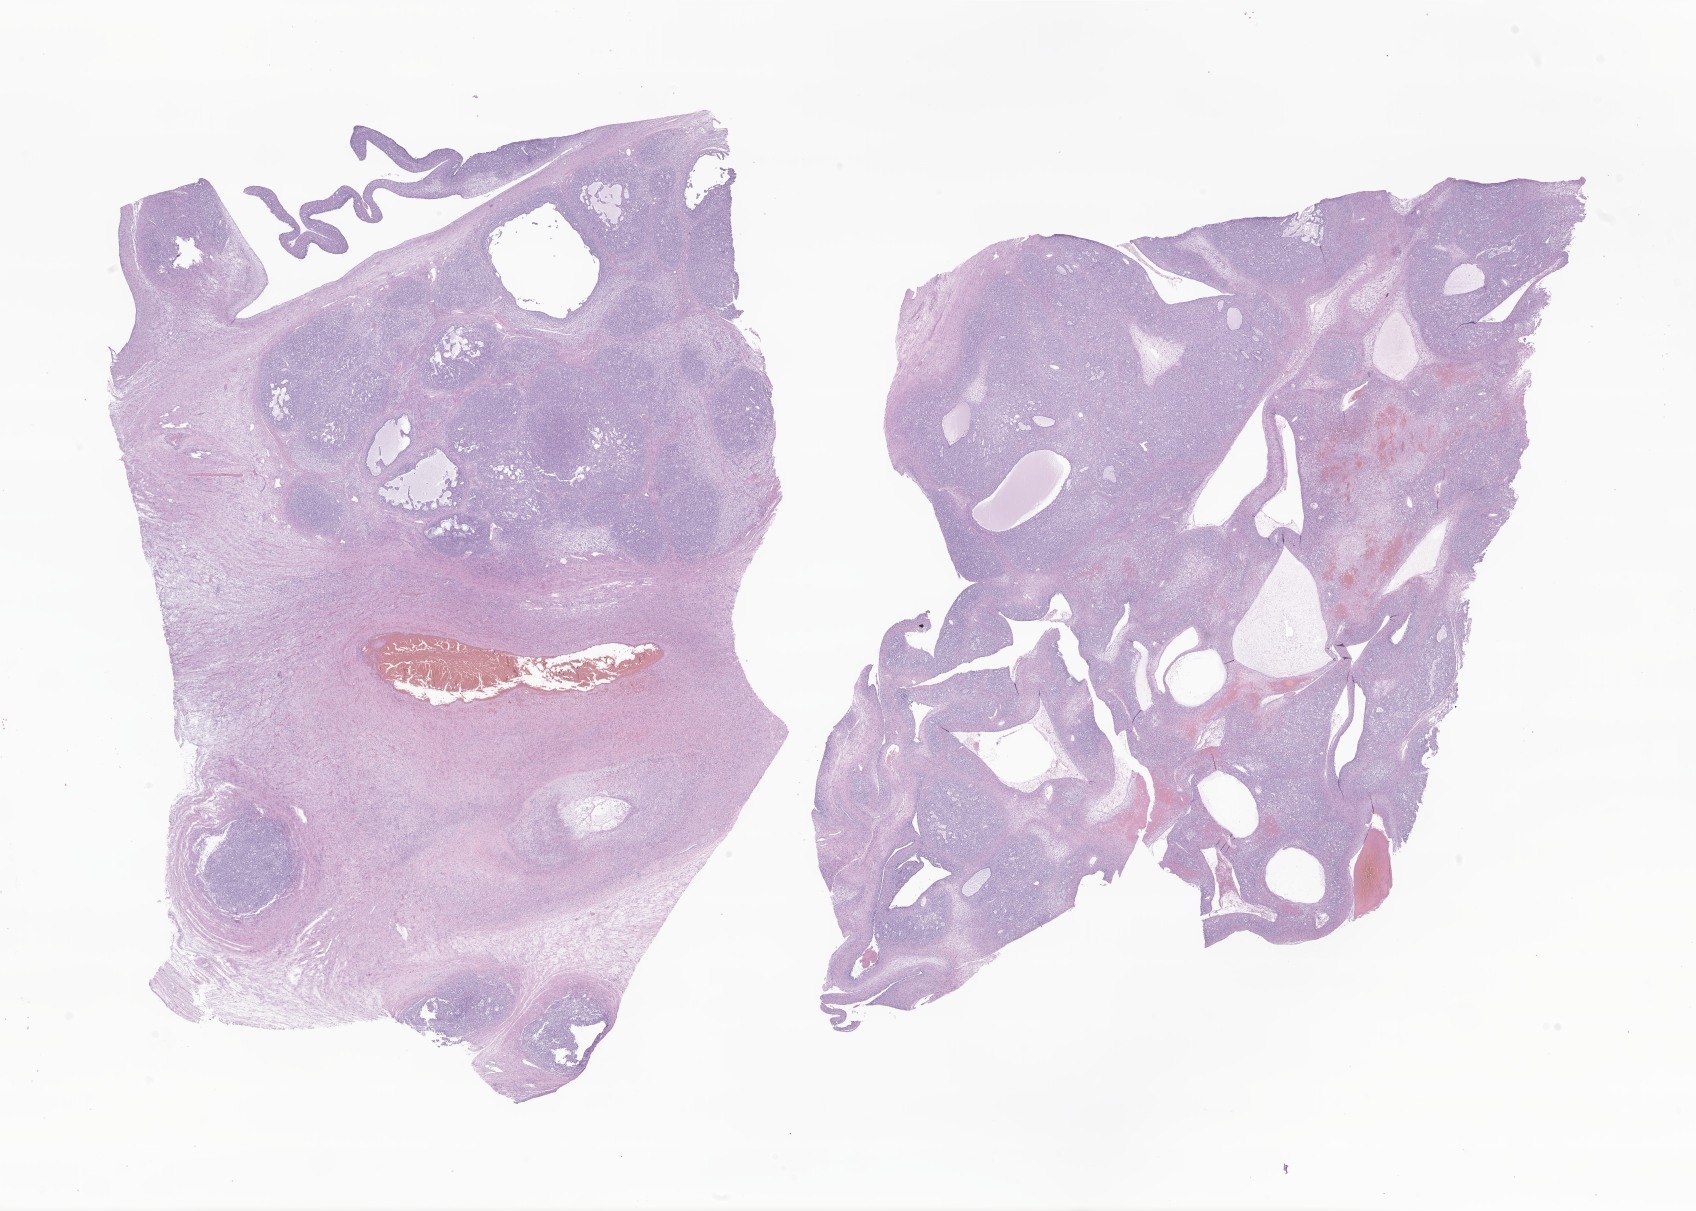
Digitized hematoxylin and eosin (H&E)-stained section of tumor tissue from the ovary — shown as a low-resolution overview of the whole scanned area (about 28.6 x 20.4 mm), FFPE section. Female patient, age 203 months.
Recorded diagnosis: Granulosa cell tumor, juvenile.